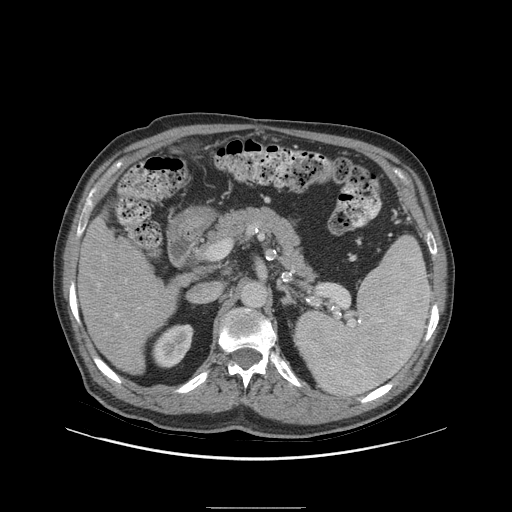
Contrast-enhanced abdominal CT (liver protocol), one axial slice; position 47 of 105 along the scan axis; soft-tissue window (W 400 / L 40 HU); 2.5 mm slice thickness; 512 × 512 image matrix. Case-level facts recorded for this patient, not image findings: diagnosis: hepatocellular carcinoma (patient treated with transarterial chemoembolisation; whether this scan precedes or follows treatment is not stated here); TNM stage (as recorded): Stage-I; Child-Pugh class: A; tumour nodularity: uninodular; tumour size: 5.1 cm.
Annotated regions visible in this slice (semi-automatically segmented with operator editing):
- liver parenchyma outside the tumour (the mass and vessels are separate outlines, so this box may not span the whole liver): bounding box <78,217,176,374> (left, top, right, bottom; pixels)
- liver vessels: <98,284,118,316>